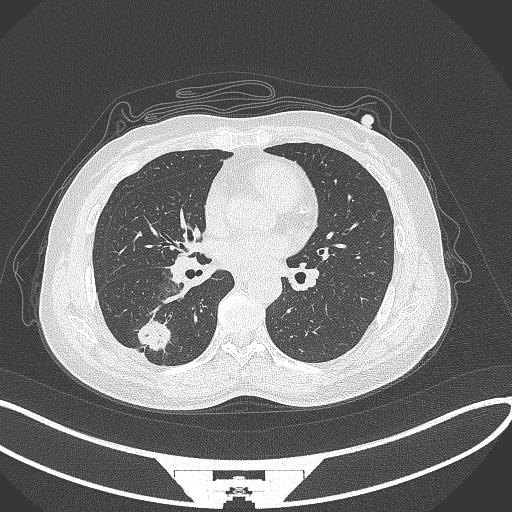
Chest CT, one axial slice. Position 143 of 352 along the scan axis. Reconstruction kernel B70f. 120 kVp. Lung window (W 1500 / L -600 HU). 1 mm slice thickness. 512 × 512 image matrix, field of view 400 × 400 mm. Female patient, age 55 years. From the clinical record (not read from this slice): clinical TNM (as recorded): T1c N1 M0.
Structures marked on this image (bounding box drawn by a radiologist):
- lung tumour (recorded histology: adenocarcinoma): box from (x=137, y=318) to (x=176, y=357) px